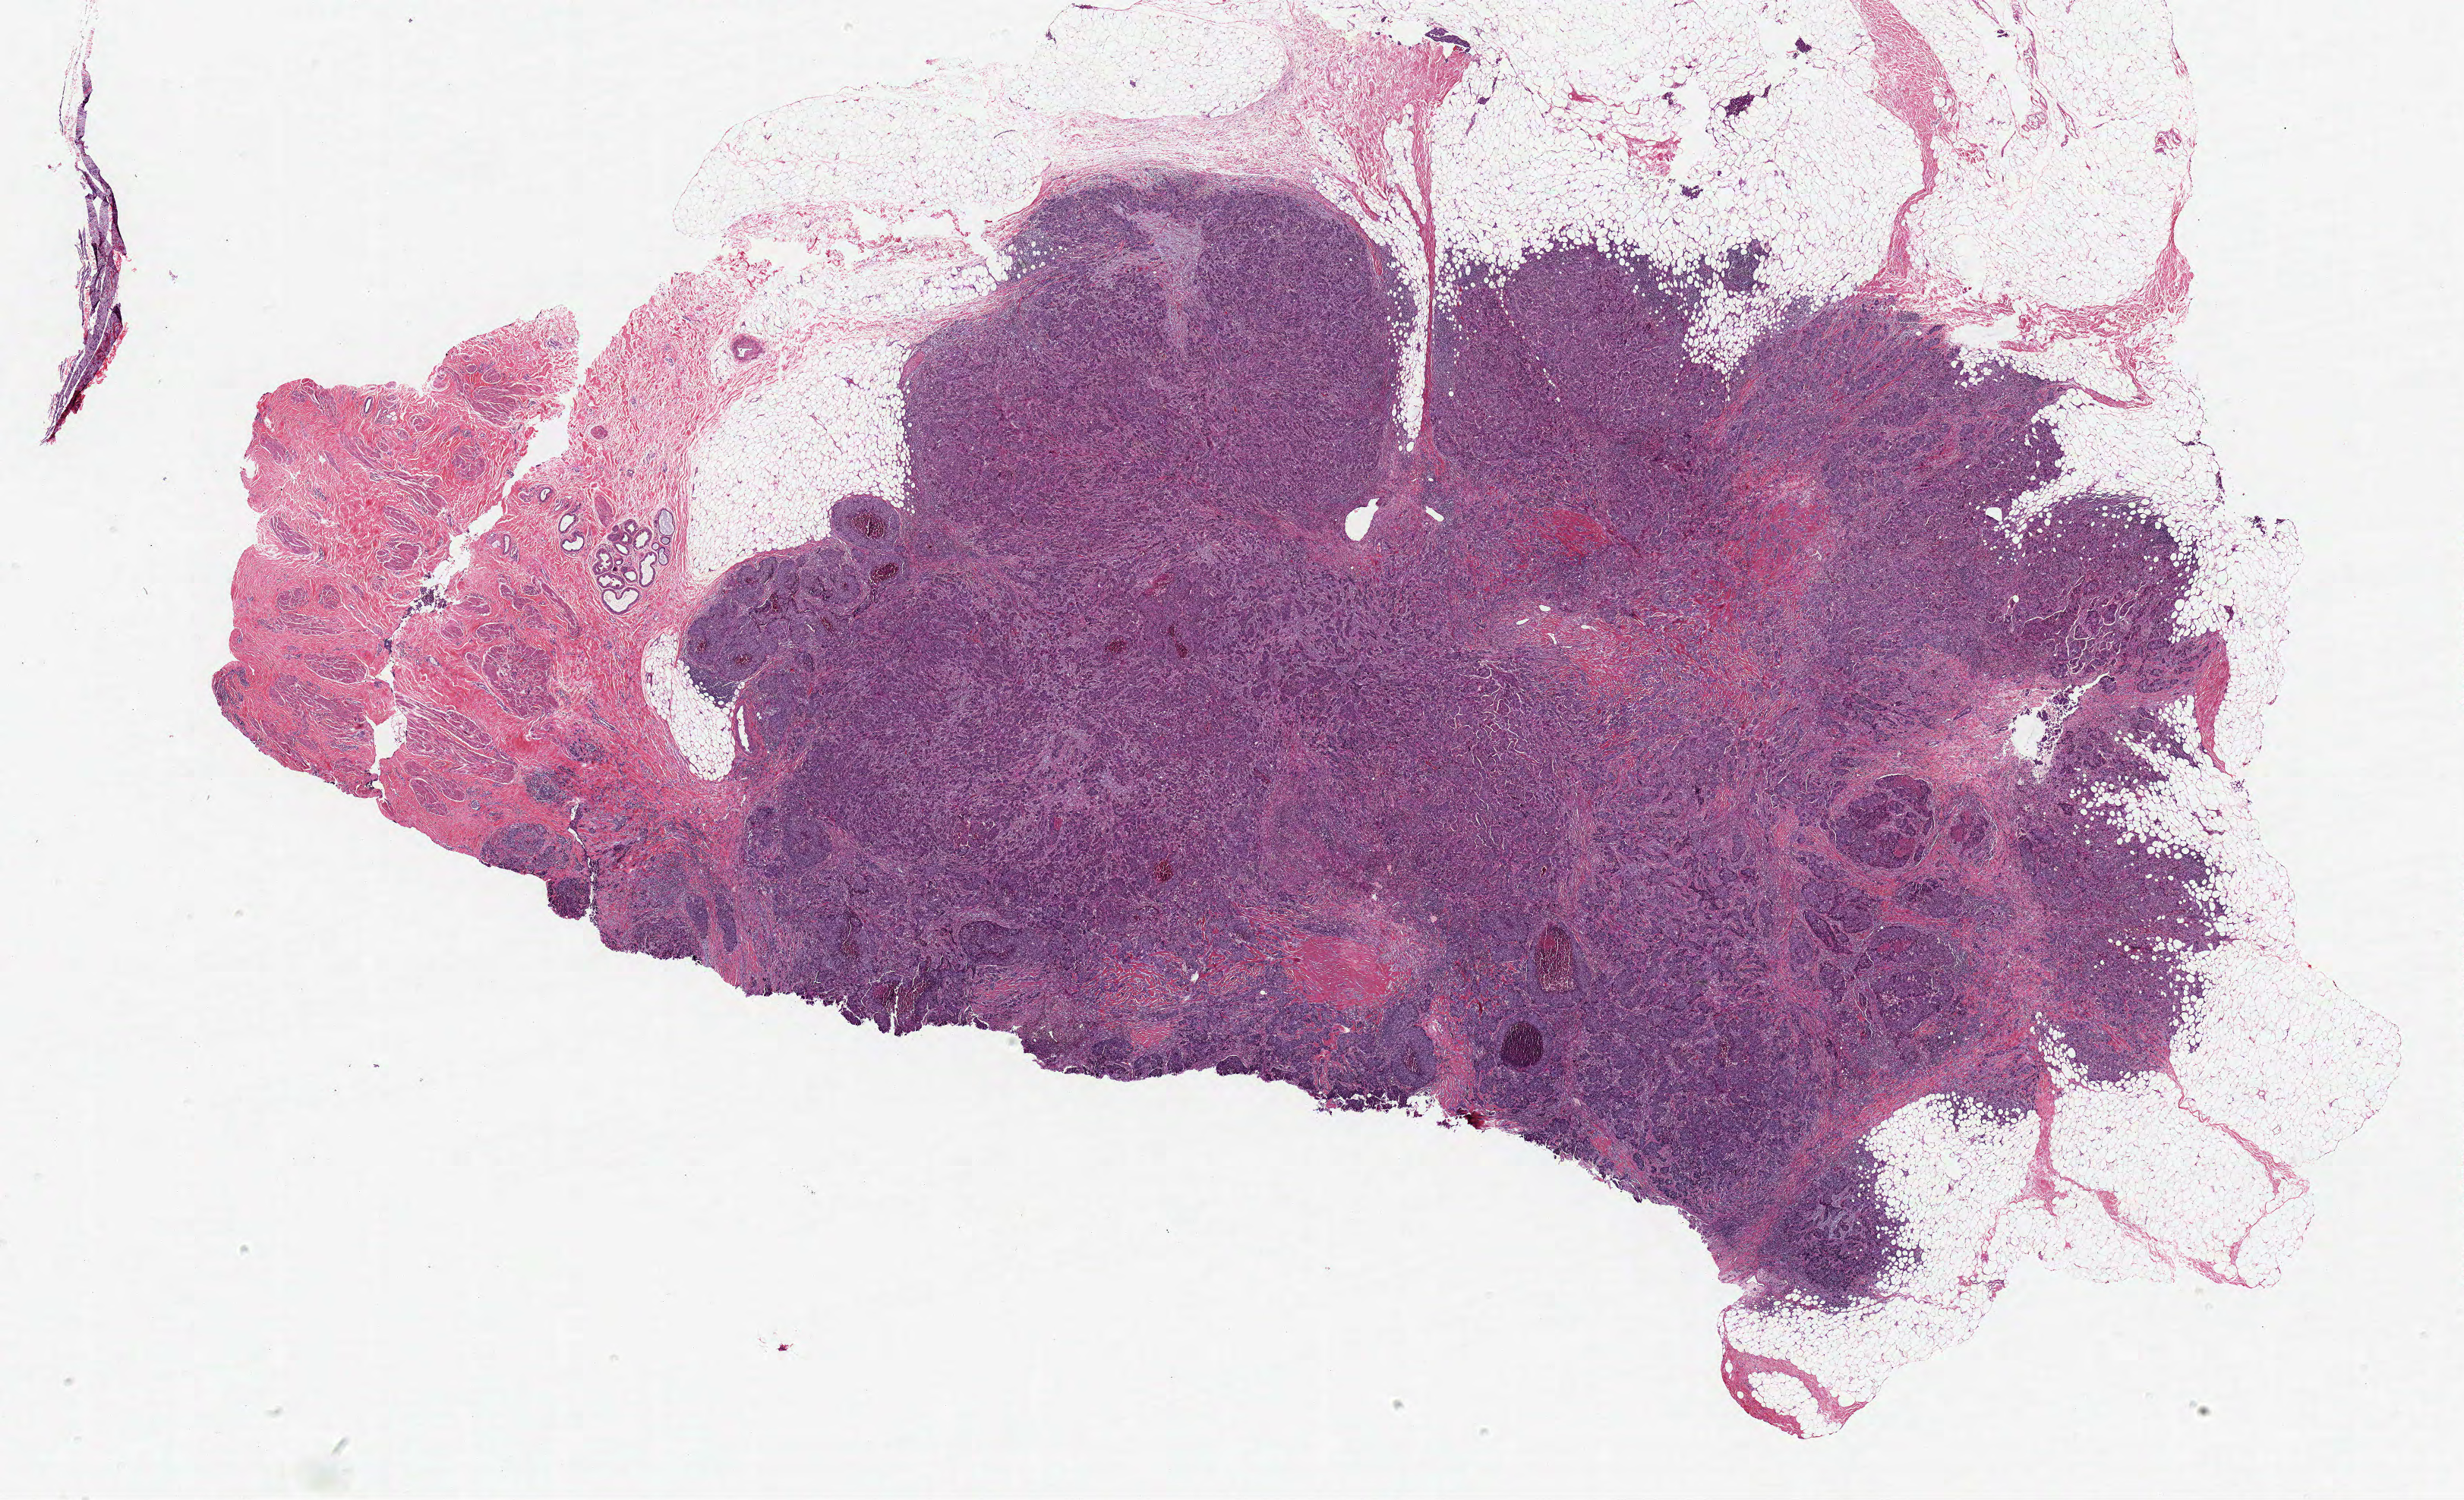
Hematoxylin and eosin (H&E) stained whole-slide image — a low-resolution overview of the entire scanned area, about 25.9 x 15.7 mm (from a 20x scan); FFPE section; sample: primary tumour, breast. Male, age 84 years at initial diagnosis.
* lymph nodes positive (case pathology): 2 of 9 examined
* diagnosis: Infiltrating duct carcinoma, NOS
* laterality: left
* AJCC pathologic stage: IIIB (6th edition)